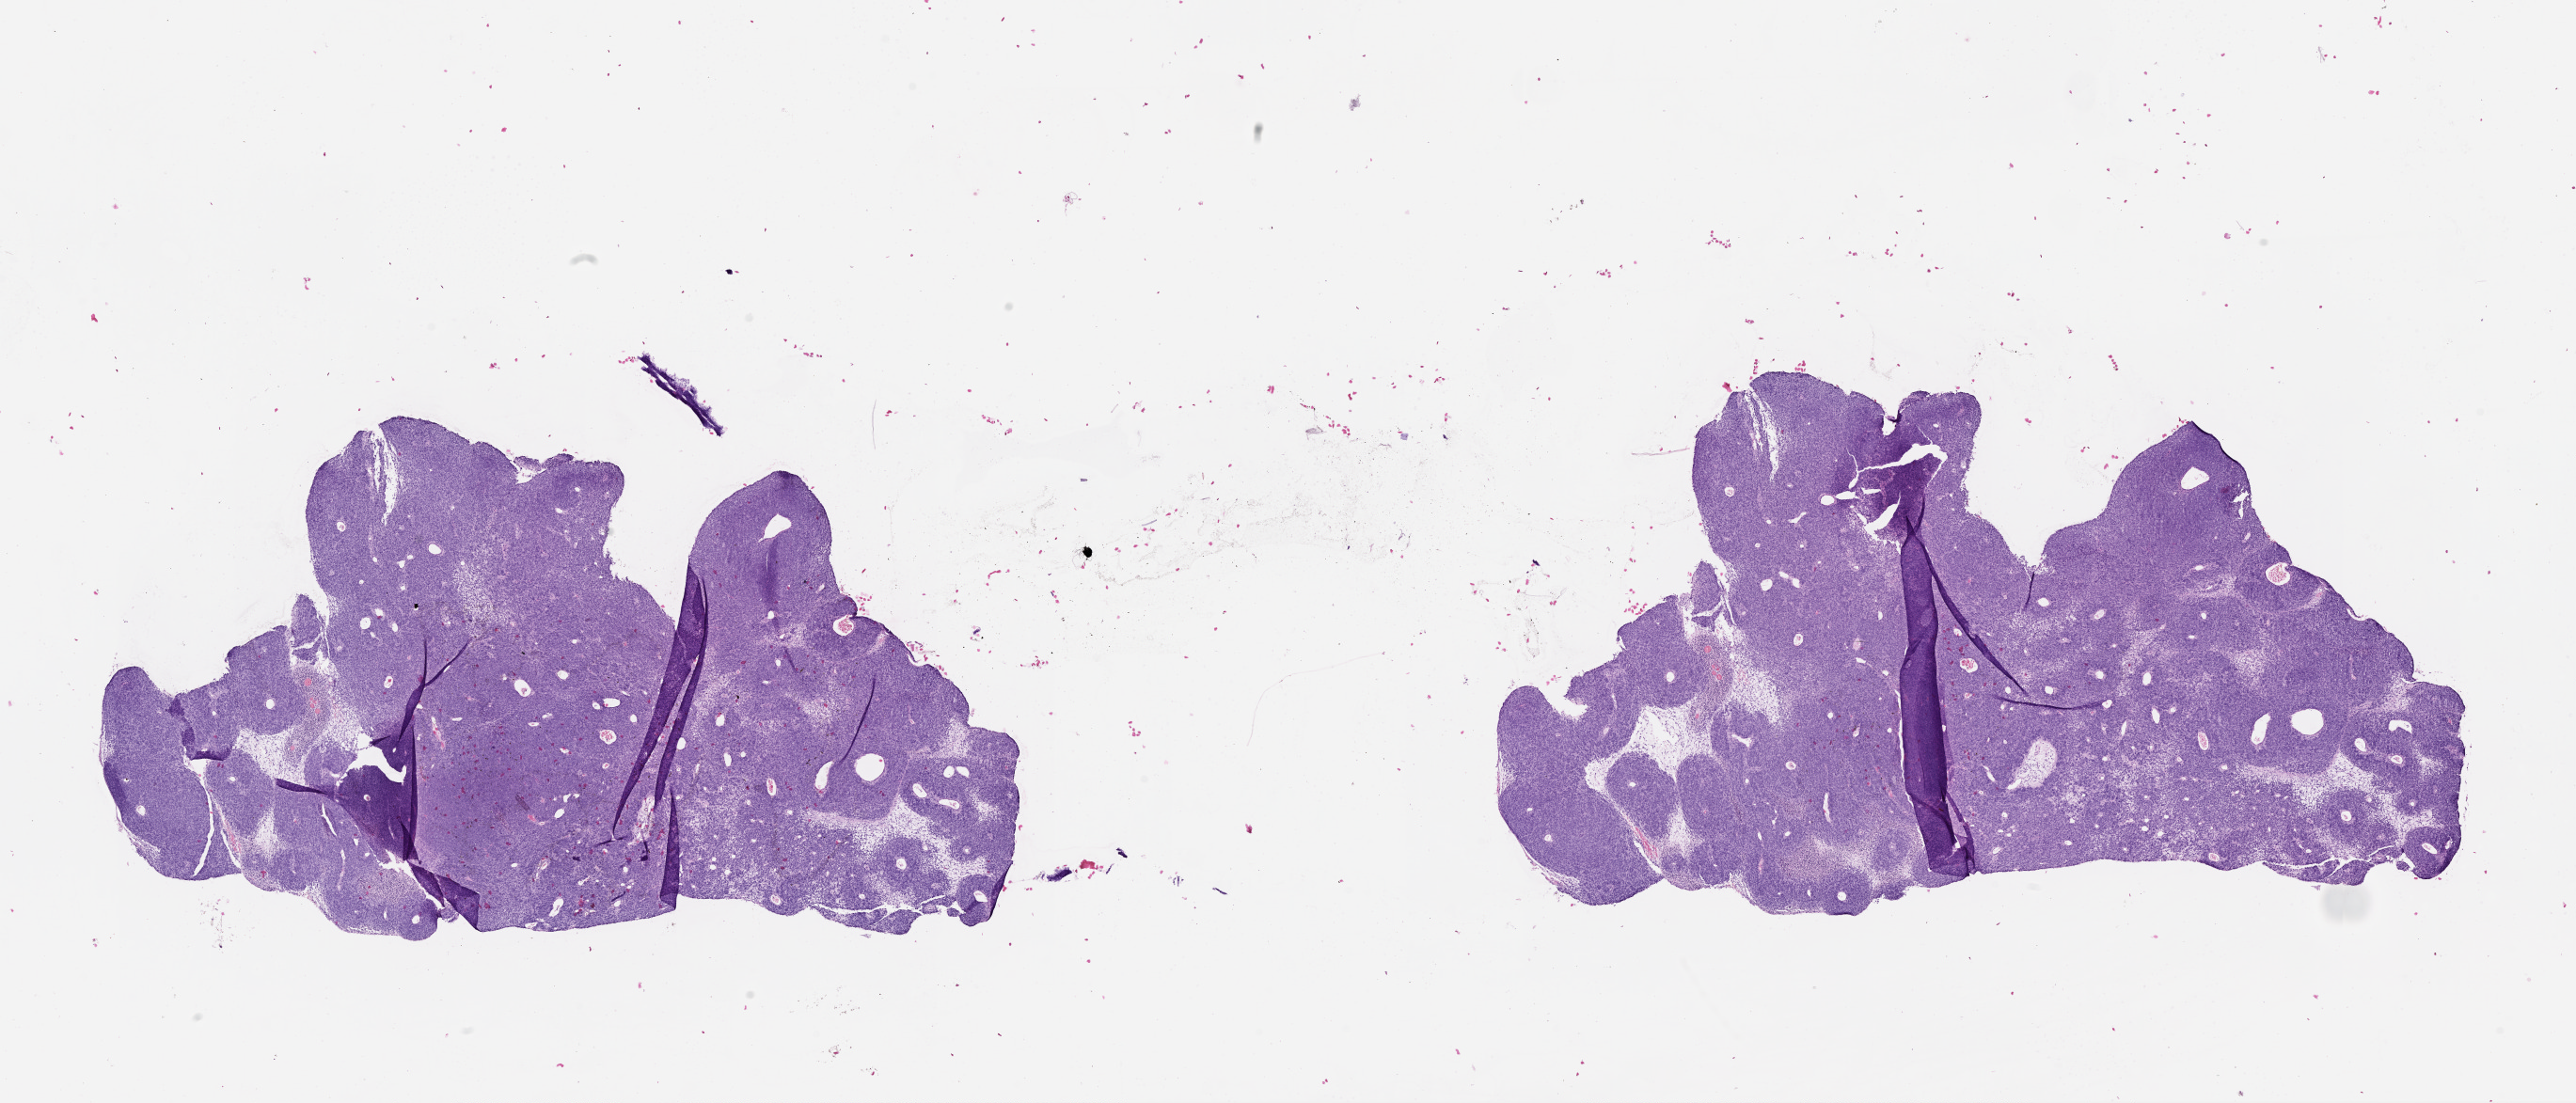
Hematoxylin and eosin (H&E) stained whole-slide image, low-resolution overview of the scanned area, about 22.0 x 9.4 mm (slide scanned at 20x). Male, 72 y/o.
Patient diagnosis: Malignant melanoma, NOS.